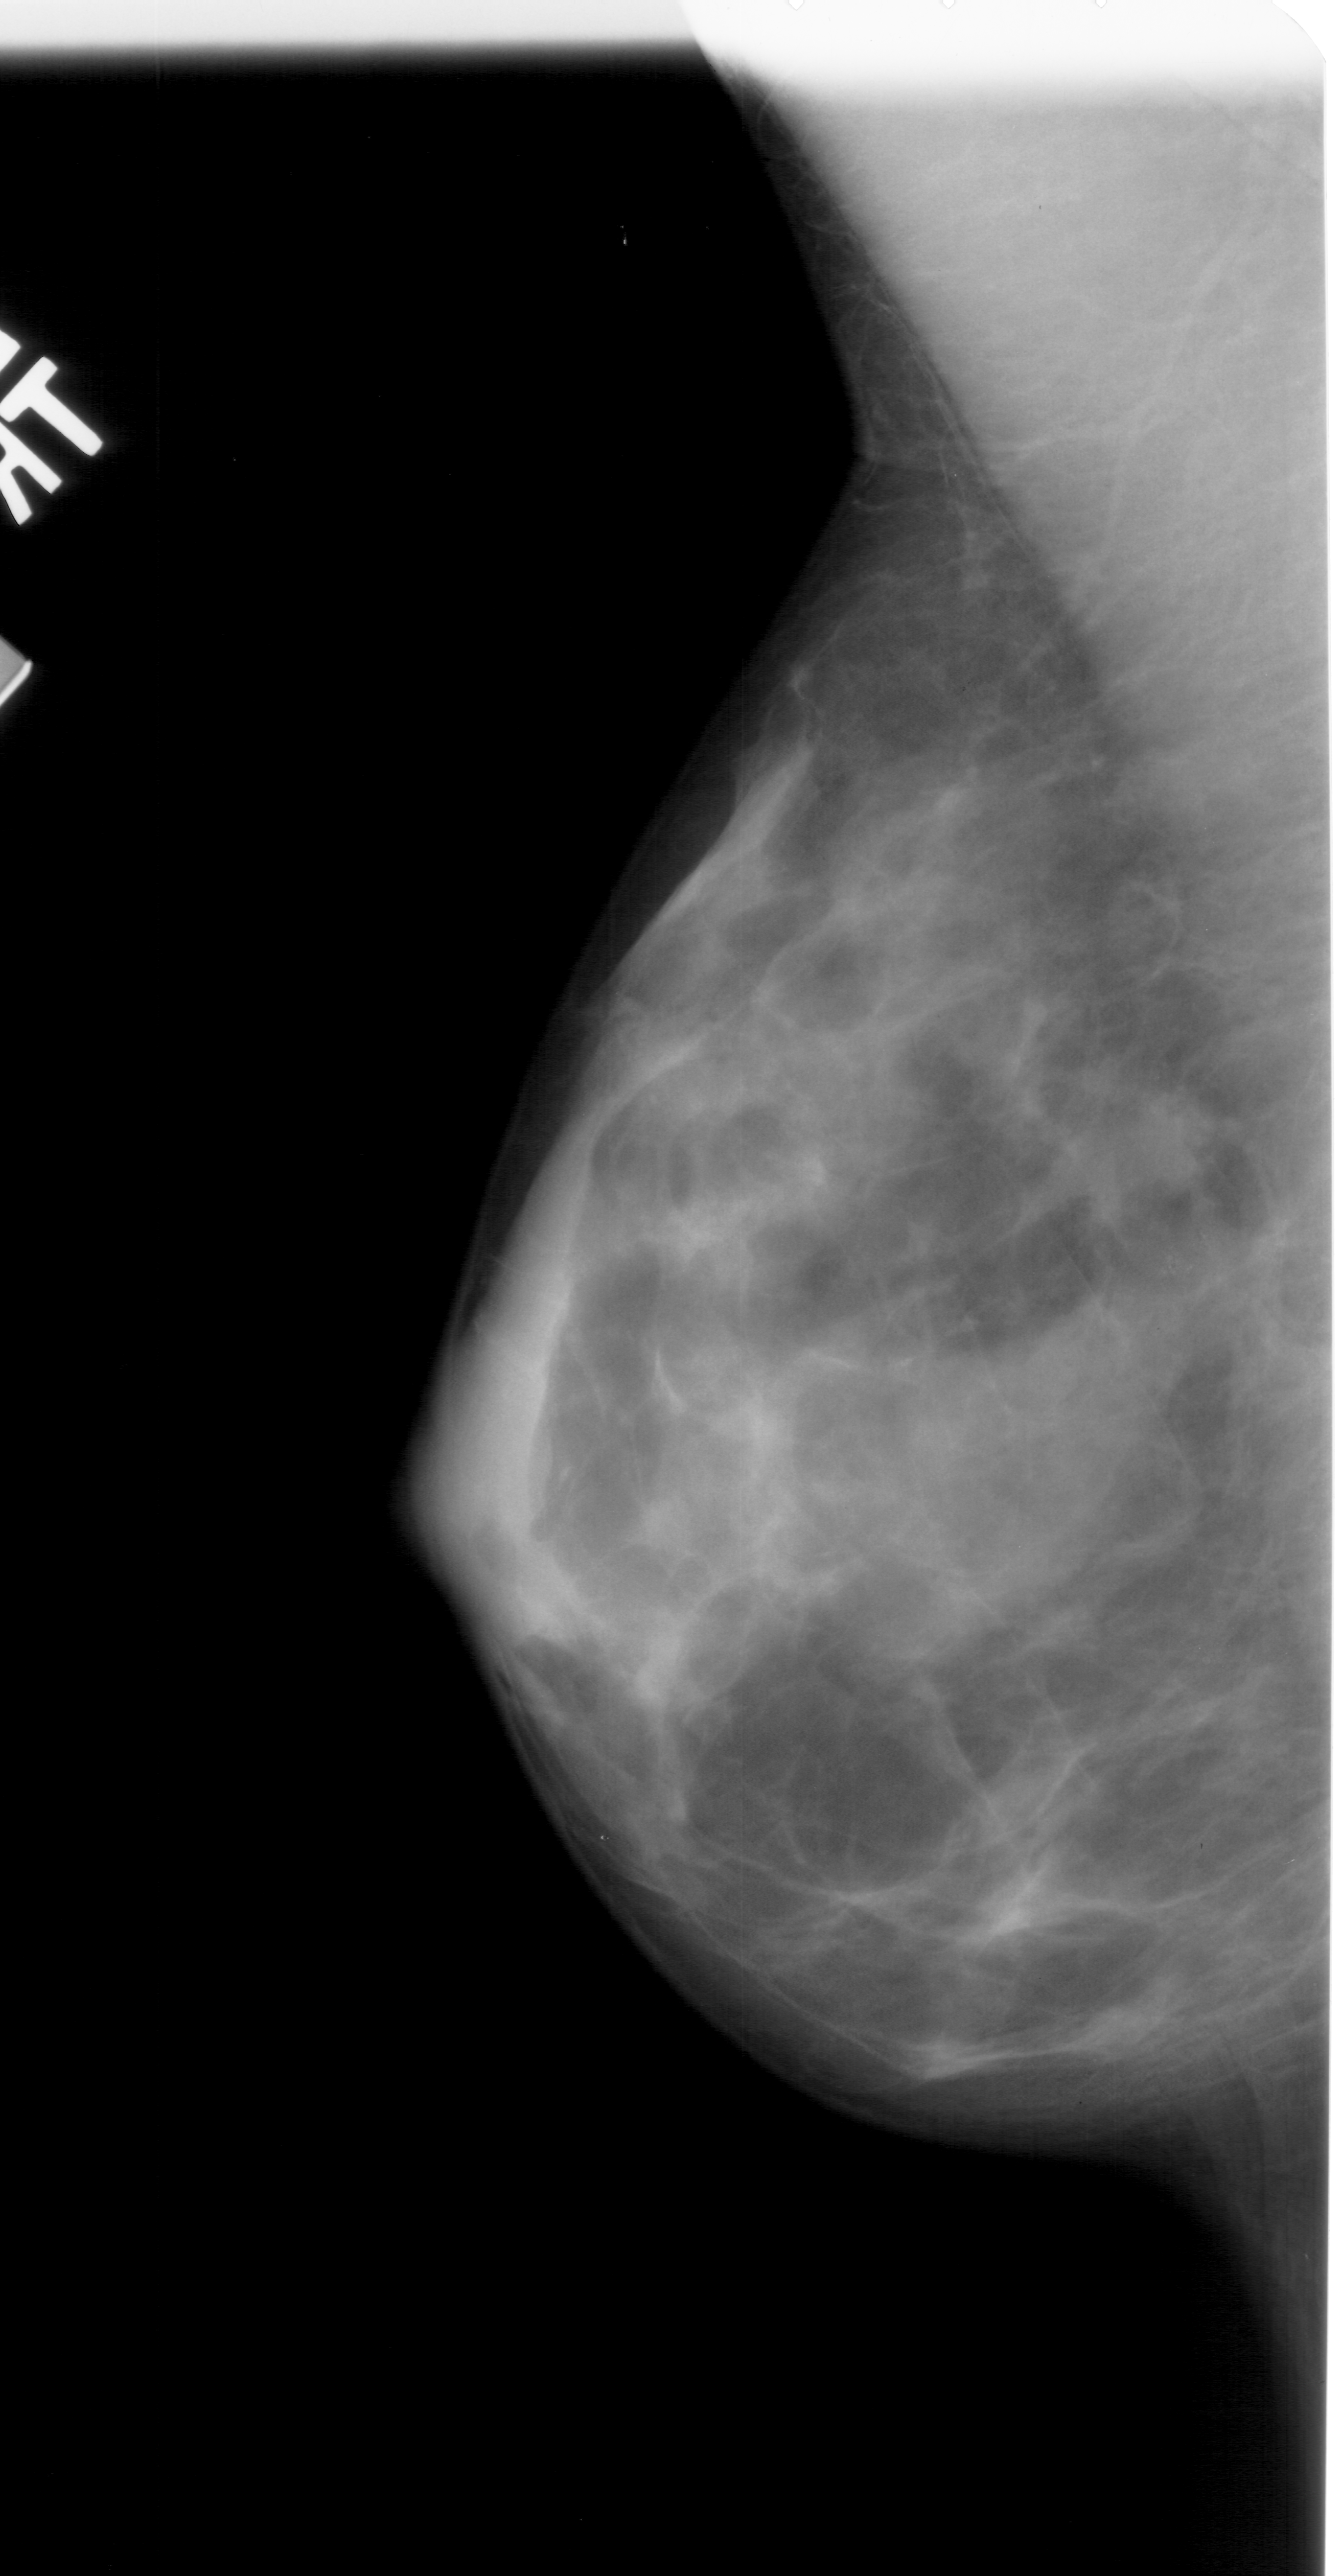
Scanned film-screen mammogram. Left breast. MLO view. Breast composition: extremely dense (BI-RADS density category 4 of 4). 1342 × 2576 image matrix.
Expert-marked regions of interest on this film, with their recorded descriptors:
- calcifications, morphology pleomorphic, distribution clustered; BI-RADS assessment category 4; pathology result (as recorded, not read from the image): benign: bounding box [x1, y1, x2, y2] px = [1144, 1212, 1232, 1295]